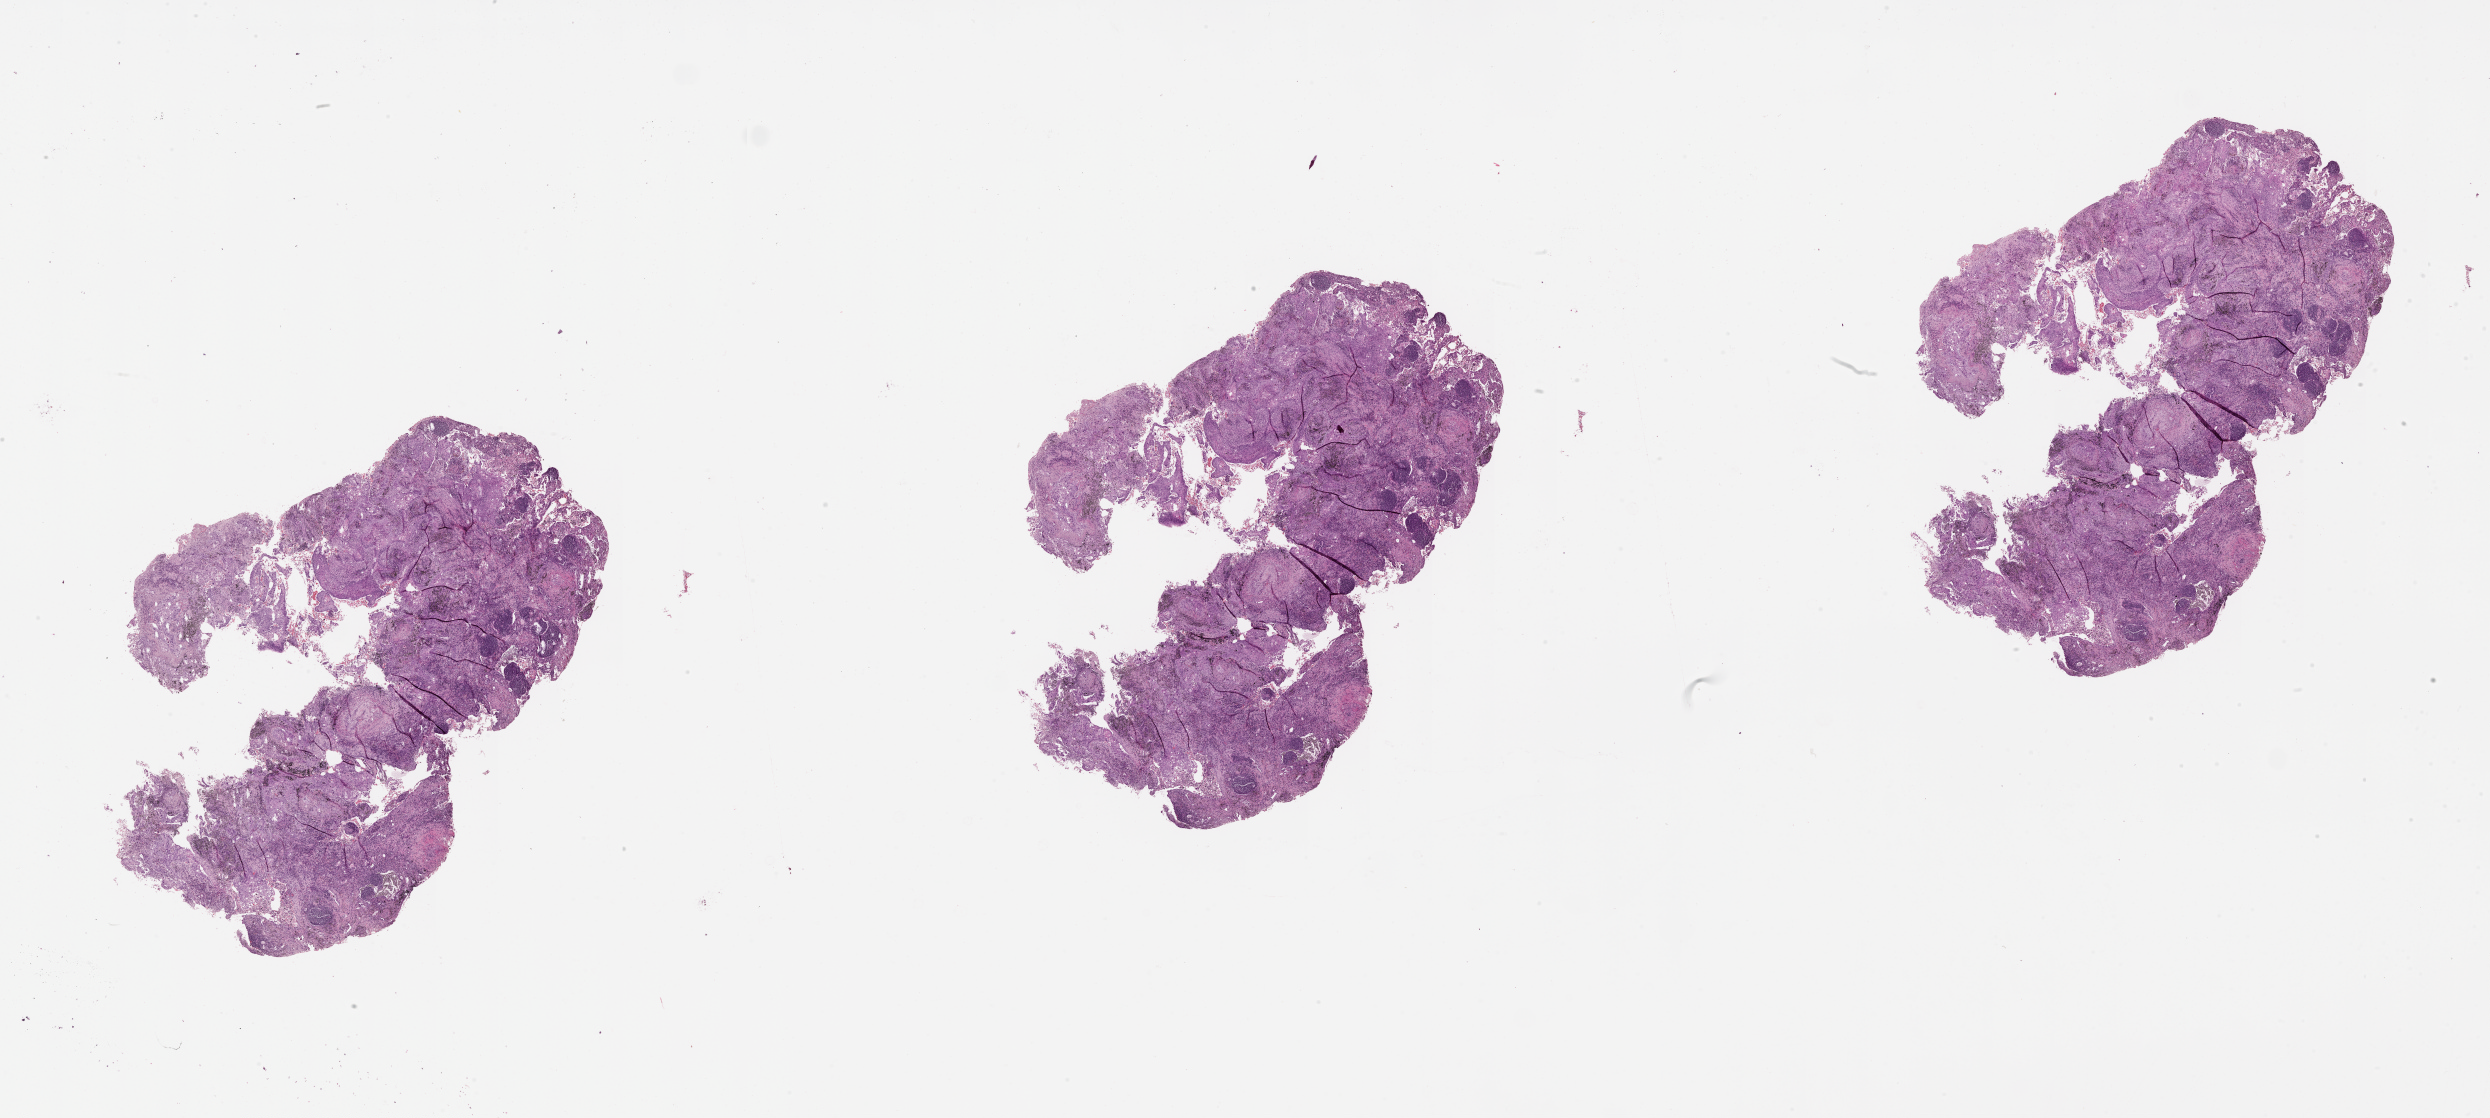
Digitized H&E tissue section (whole slide) — shown as a low-resolution overview of the whole scanned area (about 40.1 x 18.0 mm, acquisition: 20x scan). Tumour tissue sample, lung. Male, 68 y/o.
- patient diagnosis (cohort enrolment): squamous cell carcinoma (lung)